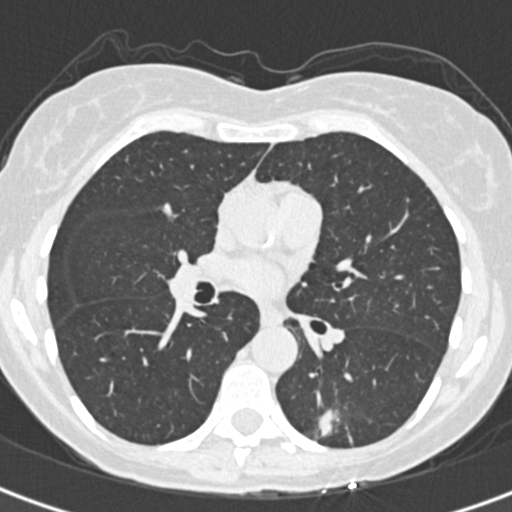
Low-dose screening chest CT, one axial slice. Slice 187 of 328 in the series (ordered by position). Reconstruction kernel B30f. 120 kVp. Lung window (W 1500 / L -600 HU). 512 × 512 image matrix, field of view 284 × 284 mm.
Structures marked on this image (expert manual segmentation):
- lesion 1 (tumor, lower lobe of left lung): bounding box <318,410,339,436> (left, top, right, bottom; pixels)